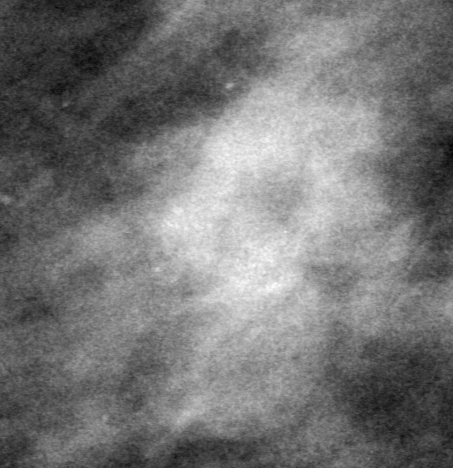
Cropped region of a digitized screen-film mammogram centred on a radiologist-marked abnormality; right breast; CC view; BI-RADS breast density category 2 (scale 1–4).
- Marked abnormality: mass, shape lobulated, margins obscured; BI-RADS assessment category 0 (incomplete: needs additional imaging); pathology (as recorded): benign.